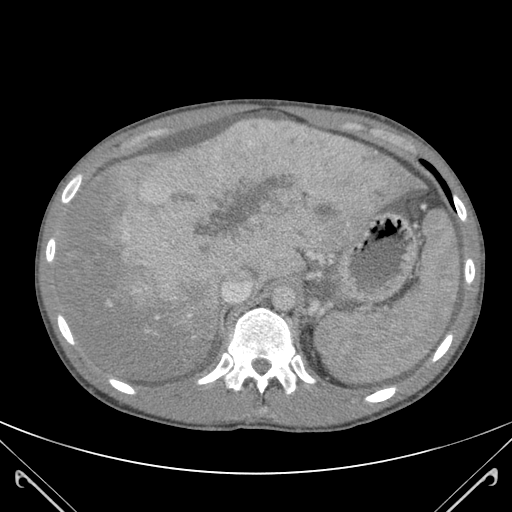
Contrast-enhanced abdominal CT (liver protocol), one axial slice. Slice 87 of 118 in the series (ordered by position). 120 kVp. Soft-tissue window (W 400 / L 40 HU). 3 mm slice thickness. 512 × 512 image matrix, field of view 380 × 380 mm. Case-level facts recorded for this patient, not image findings: diagnosis: hepatocellular carcinoma (patient treated with transarterial chemoembolisation; whether this scan precedes or follows treatment is not stated here); TNM stage (as recorded): Stage-IIIB; Child-Pugh class: A.
Outlined on this slice (semi-automatic segmentation, software-assisted and operator-edited):
- abdominal aorta: bounding box [x1, y1, x2, y2] px = [273, 286, 298, 310]
- liver parenchyma outside the tumour (the mass and vessels are separate outlines, so this box may not span the whole liver): [61, 122, 423, 378]
- mass: [97, 124, 414, 326]
- liver vessels: [108, 123, 304, 306]